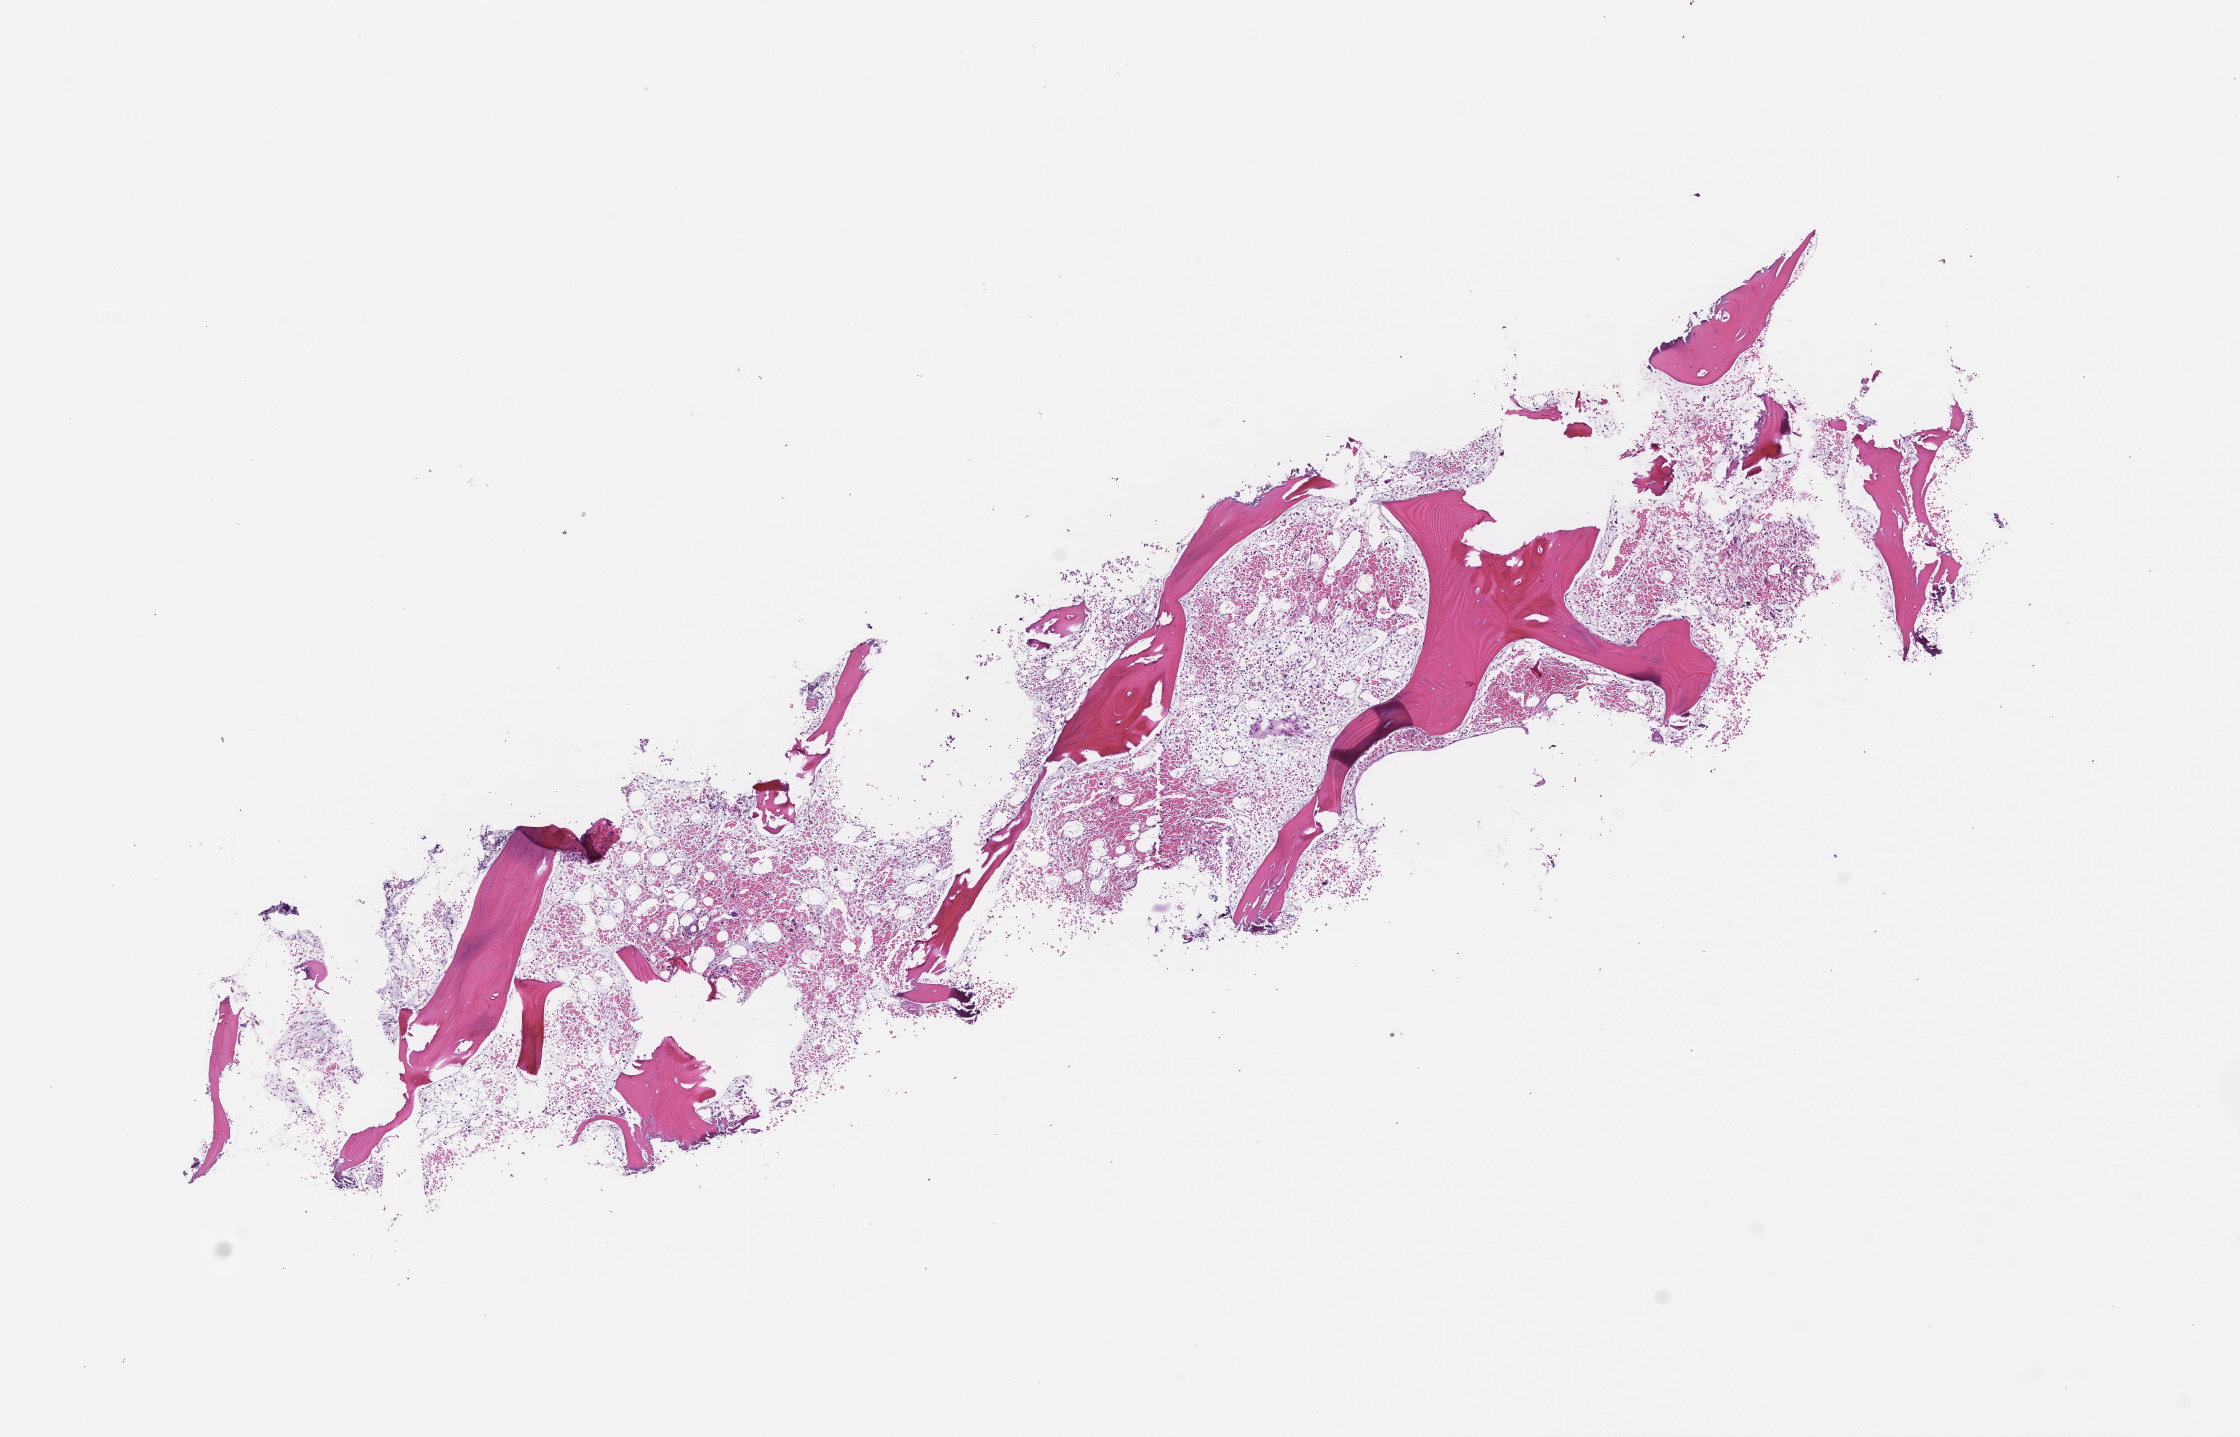
Digitized H&E-stained section, low-resolution overview of the scanned area, about 9.0 x 5.8 mm. Formalin-fixed, paraffin-embedded (FFPE) tissue. Tissue site: bone marrow. Collected on treatment. Patient: male.
• this section: primary tumor
• diagnosis: Acute Myeloid Leukemia Not Otherwise Specified